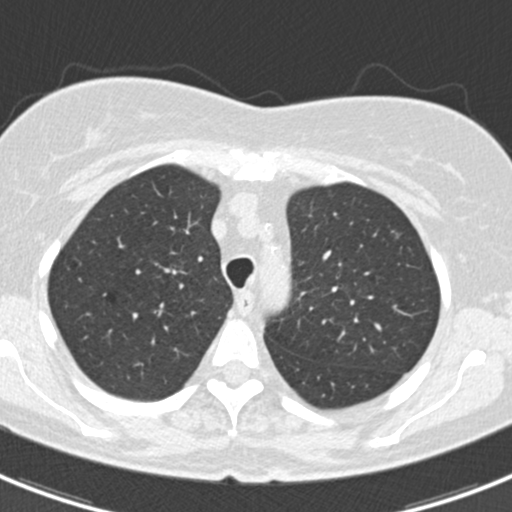
Chest CT (low-dose screening protocol), one axial image. First (baseline) screen. Lung window (W 1500 / L -600 HU). 2 mm slice thickness. Slice 50 of 184 in the series. 512 × 512 image matrix. Female, age 60 years at enrolment.
Expert-annotated lung lesion, bounding box [x1, y1, x2, y2] px = [374, 224, 419, 259]. The screening reader recorded 3 non-calcified nodules or masses ≥4 mm on this exam (lingula, left lower lobe, lingula); which of them this box marks is not recorded. Official screen result: positive, change unspecified: nodule(s) >= 4 mm or enlarging nodule(s), mass(es), or other non-specific abnormalities suspicious for lung cancer. Participant outcome: lung cancer diagnosed 886 days after this screen (after the third annual screen) — non-small cell carcinoma, left upper lobe, poorly differentiated (G3), stage IB (AJCC 6th edition), 7 mm at pathology.